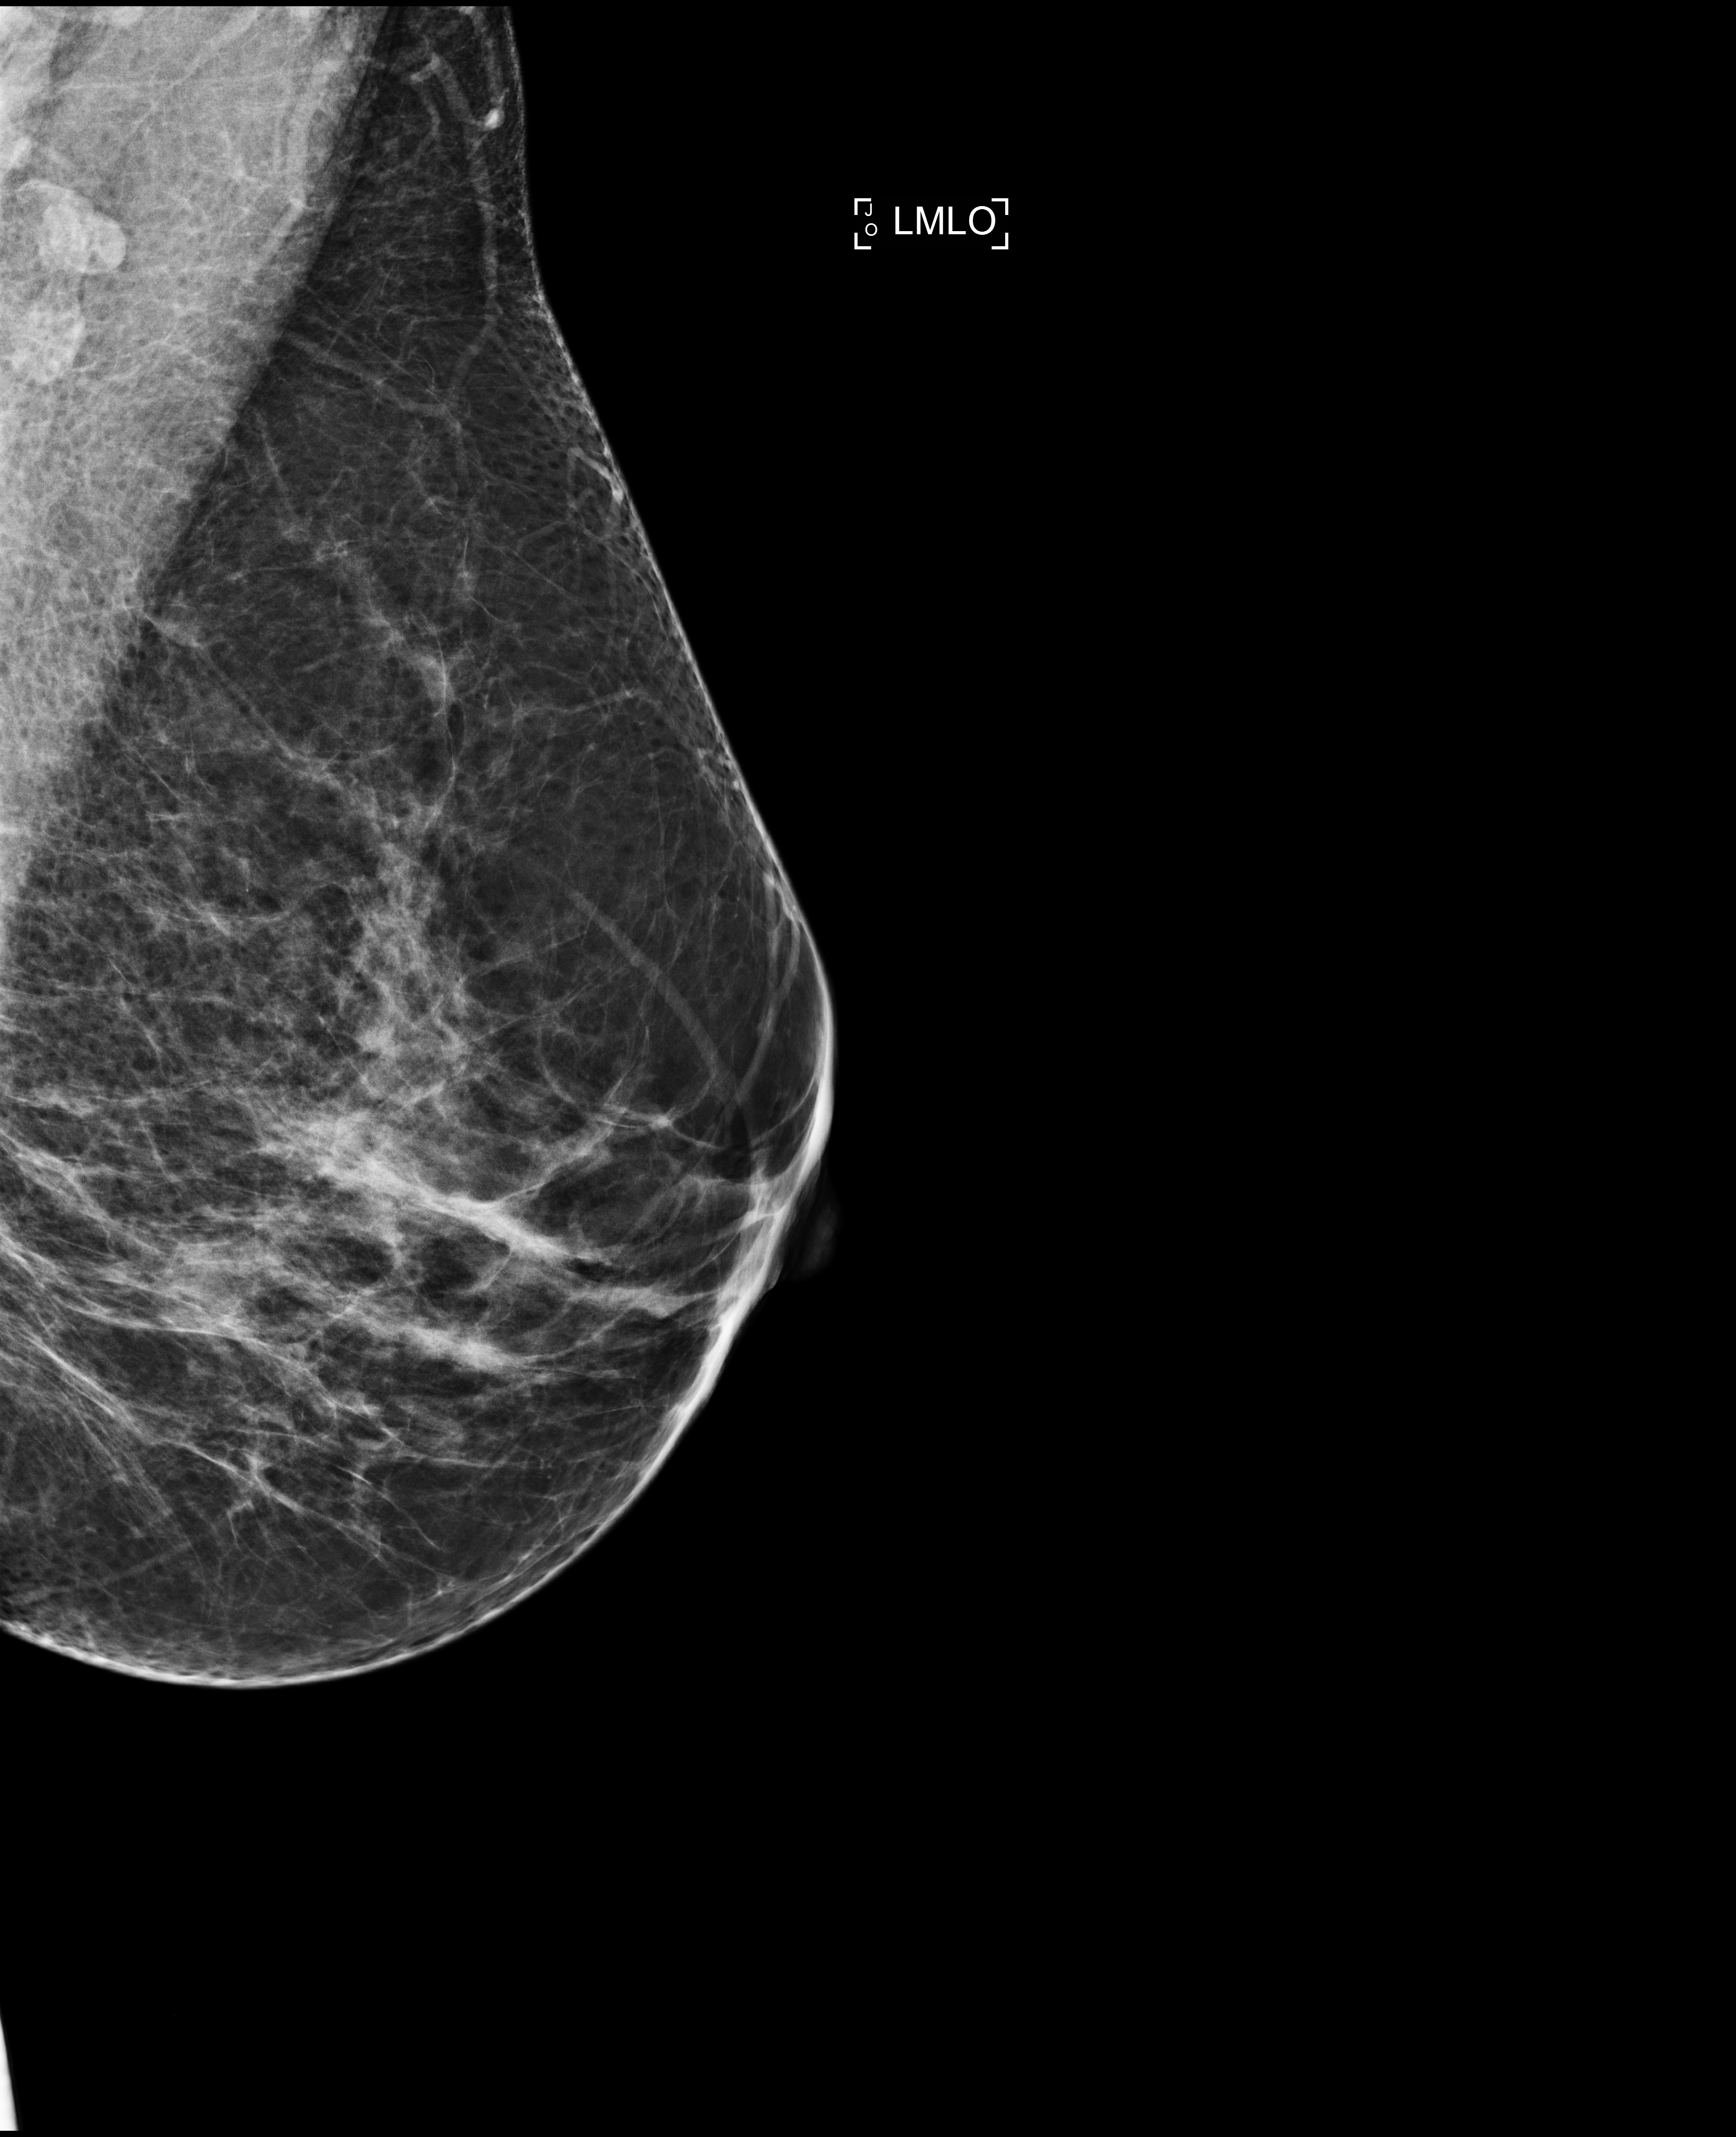
Annual screening mammography examination; compressed breast thickness 70 mm. Female patient, age 48 years.
Image type: full-field digital mammogram. Breast: left. Projection: MLO view.